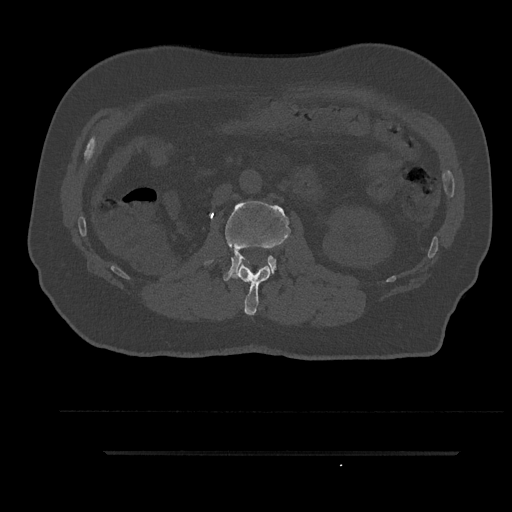
CT including the spine, one axial slice; slice 136 of 797 in the series (ordered by position); reconstruction kernel Br40s/3; 120 kVp; bone window (W 1800 / L 400 HU); 512 × 512 image matrix, field of view 432 × 432 mm. Patient: male, 63 years. Case-level facts recorded for this patient, not image findings: primary cancer: renal; vertebrae with lytic lesions (as recorded): T8.
Outlined on this slice (semi-automatic segmentation, software-assisted and operator-edited):
- L1 vertebra: bounding box <232,264,271,316> (left, top, right, bottom; pixels)
- L2 vertebra: <206,201,291,281>